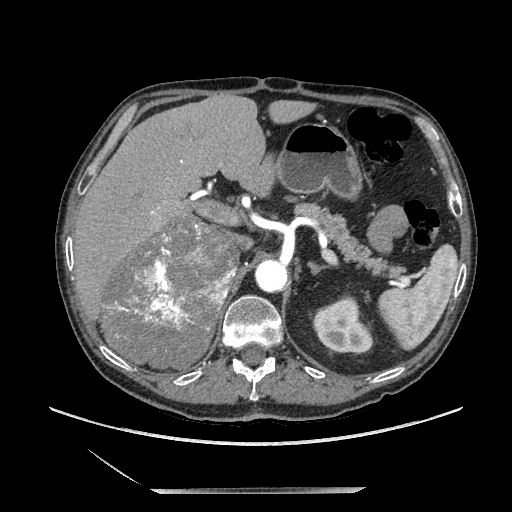
Contrast-enhanced abdominal CT, one axial slice. Slice 138 of 243 in the series (ordered by position). Soft-tissue window (W 400 / L 40 HU). 1.25 mm slice thickness. 512 × 512 image matrix, field of view 420 × 420 mm. Male patient. Case-level facts recorded for this patient, not image findings: diagnosis: adrenocortical carcinoma; tumour side: right adrenal; tumour size at pathology: 16 cm.
Annotated regions visible in this slice (semi-automatically segmented with operator editing):
- mass: bounding box (x1, y1, x2, y2) in pixels: (106, 222, 237, 367)